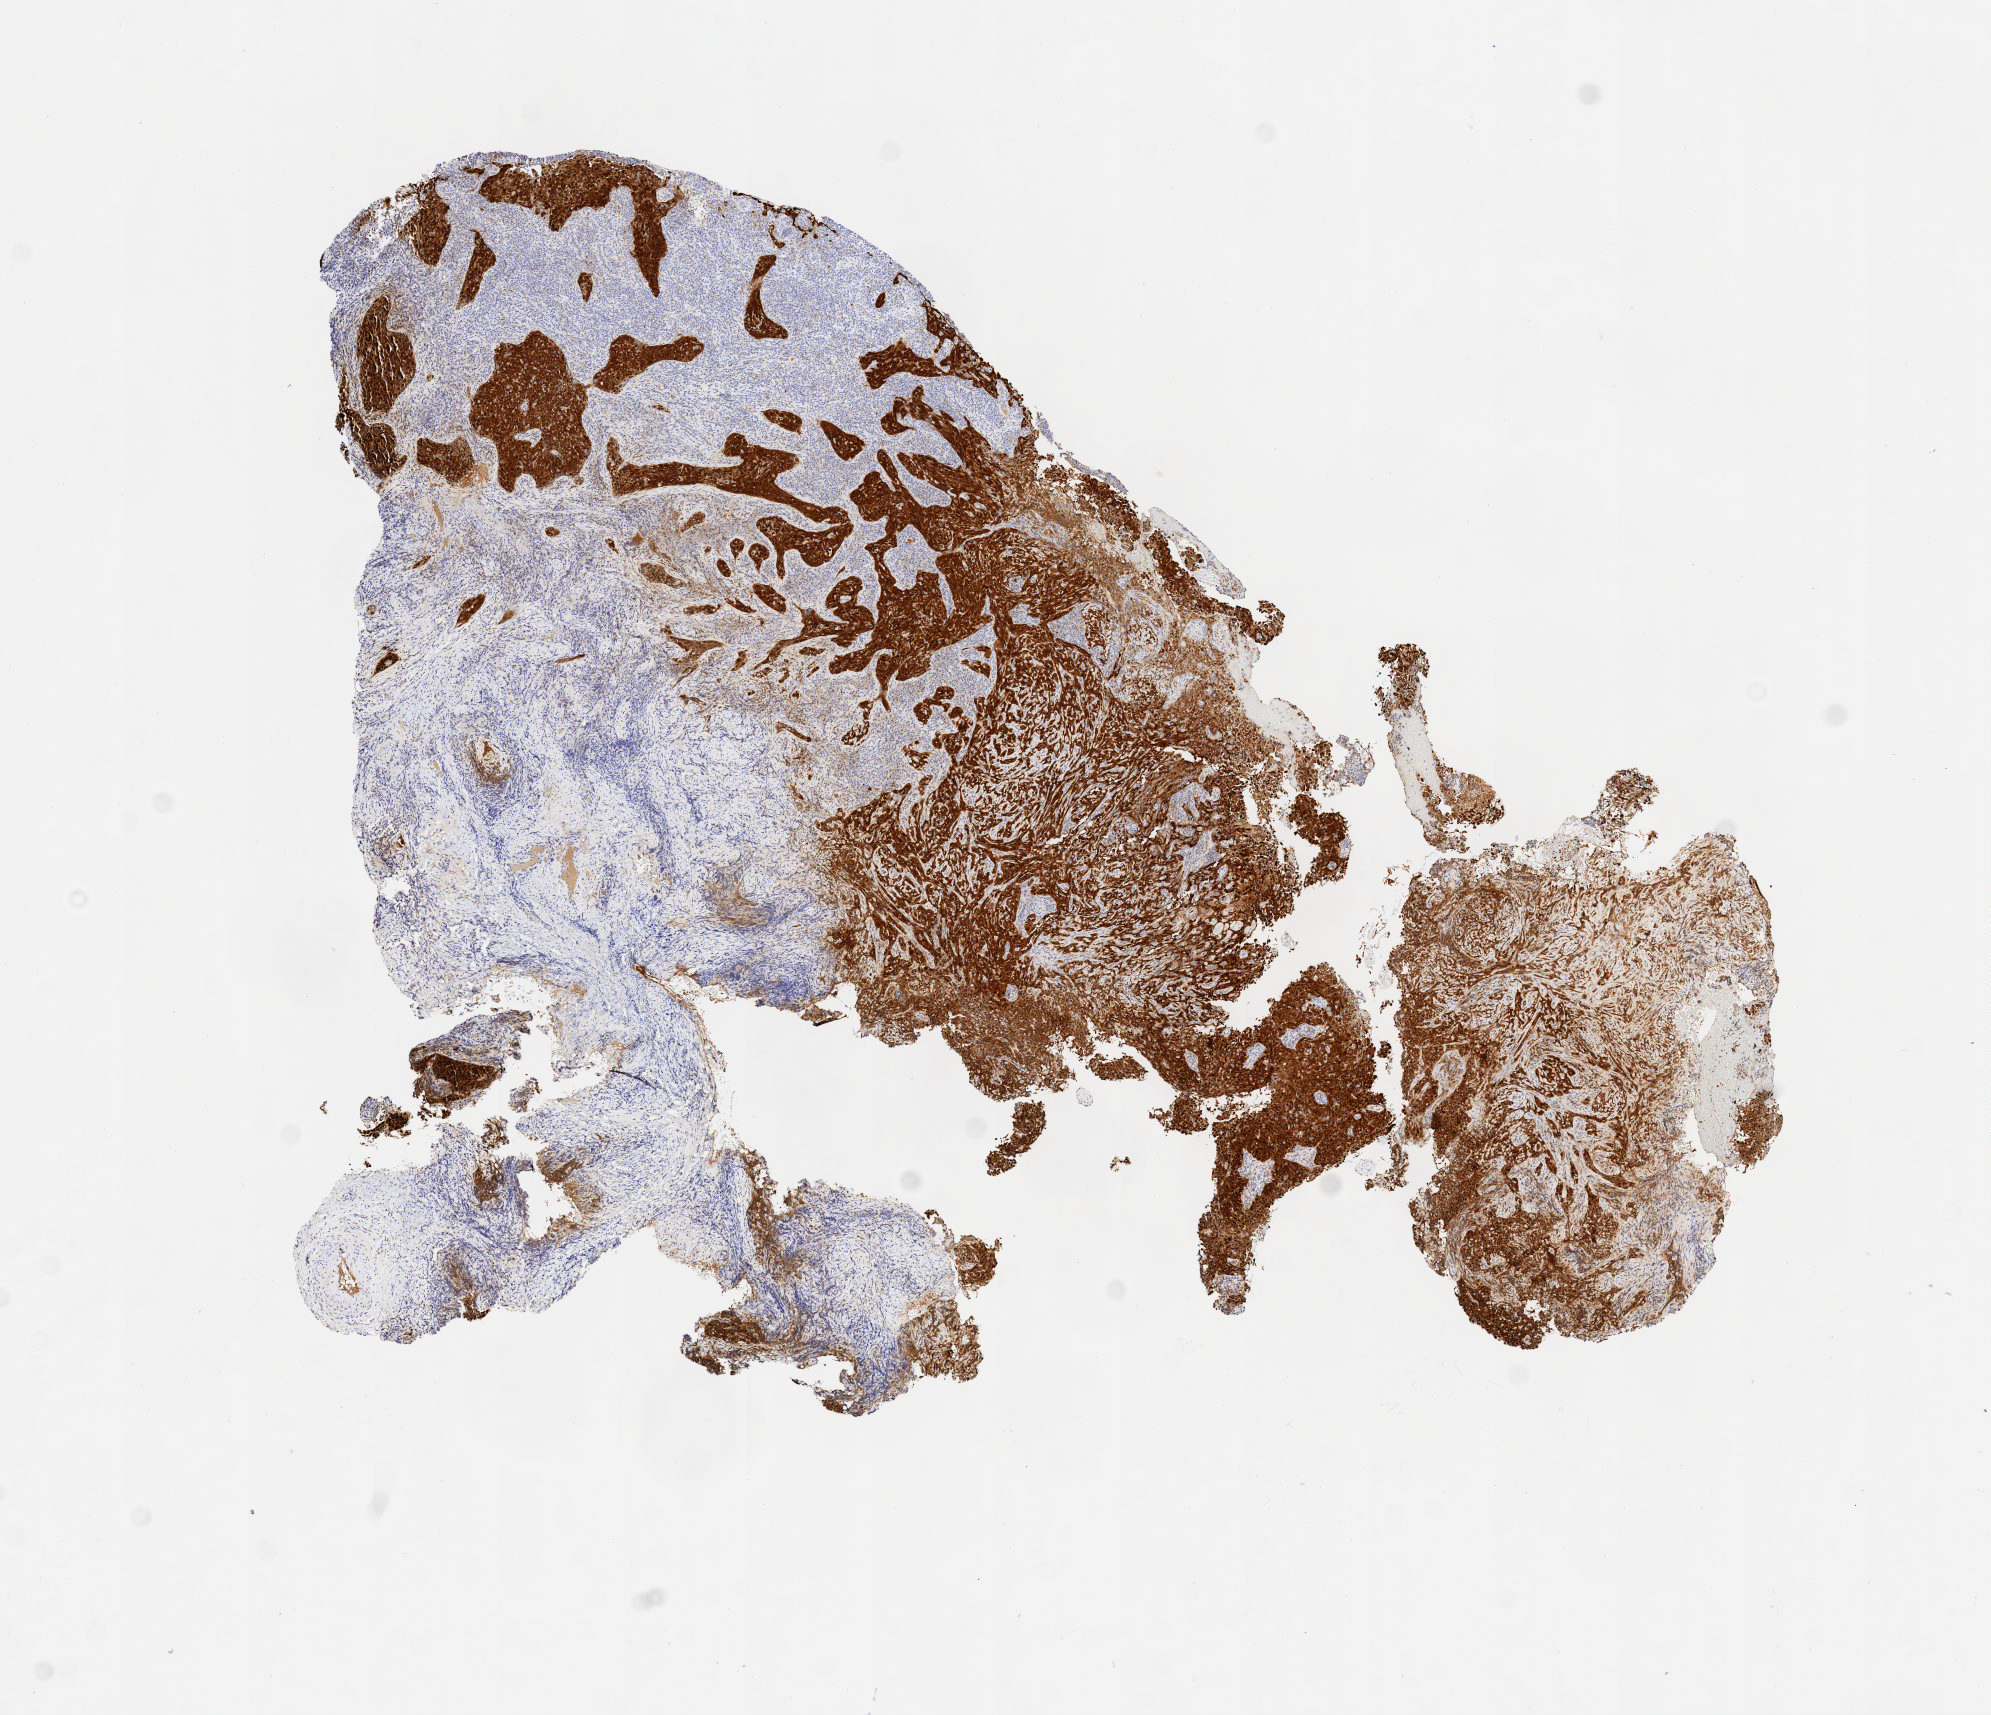
Whole-slide image, immunohistochemical stain for p16 (p16INK4a) — whole scanned area (about 8.1 x 6.9 mm) shown as a low-resolution overview; tumor tissue; anatomic site: cervix. Patient female; age 35 years.
Histologic diagnosis: Squamous cell carcinoma, large cell, nonkeratinizing, NOS.